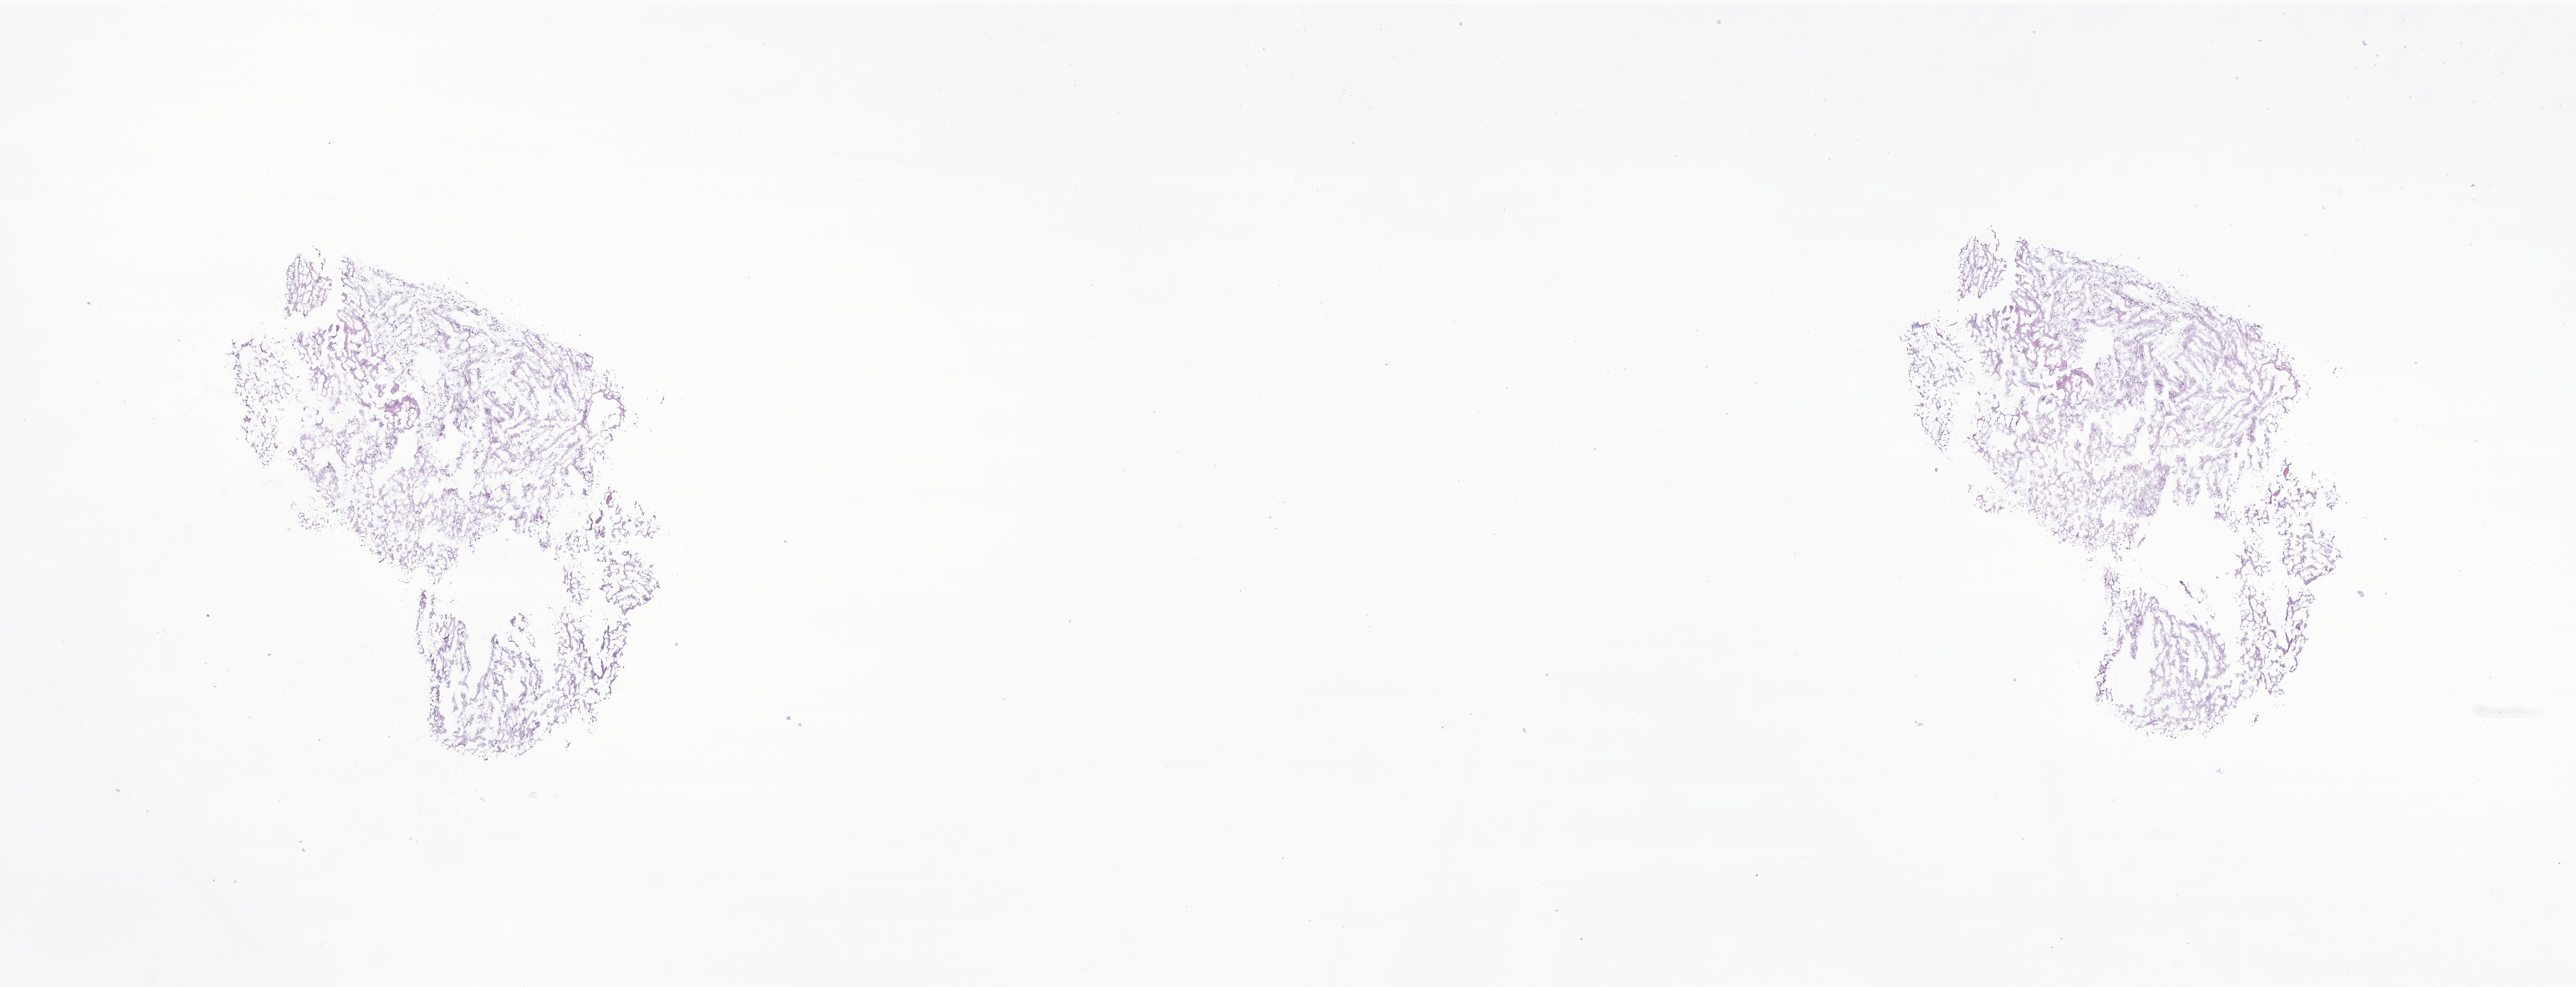
Digitized haematoxylin and eosin-stained section of tumor tissue from the cerebellum — whole scanned area (about 20.3 x 7.8 mm) shown as a low-resolution overview, frozen section. Patient female; age 233 months (19 years 5 months).
Recorded diagnosis: Glioma, malignant.